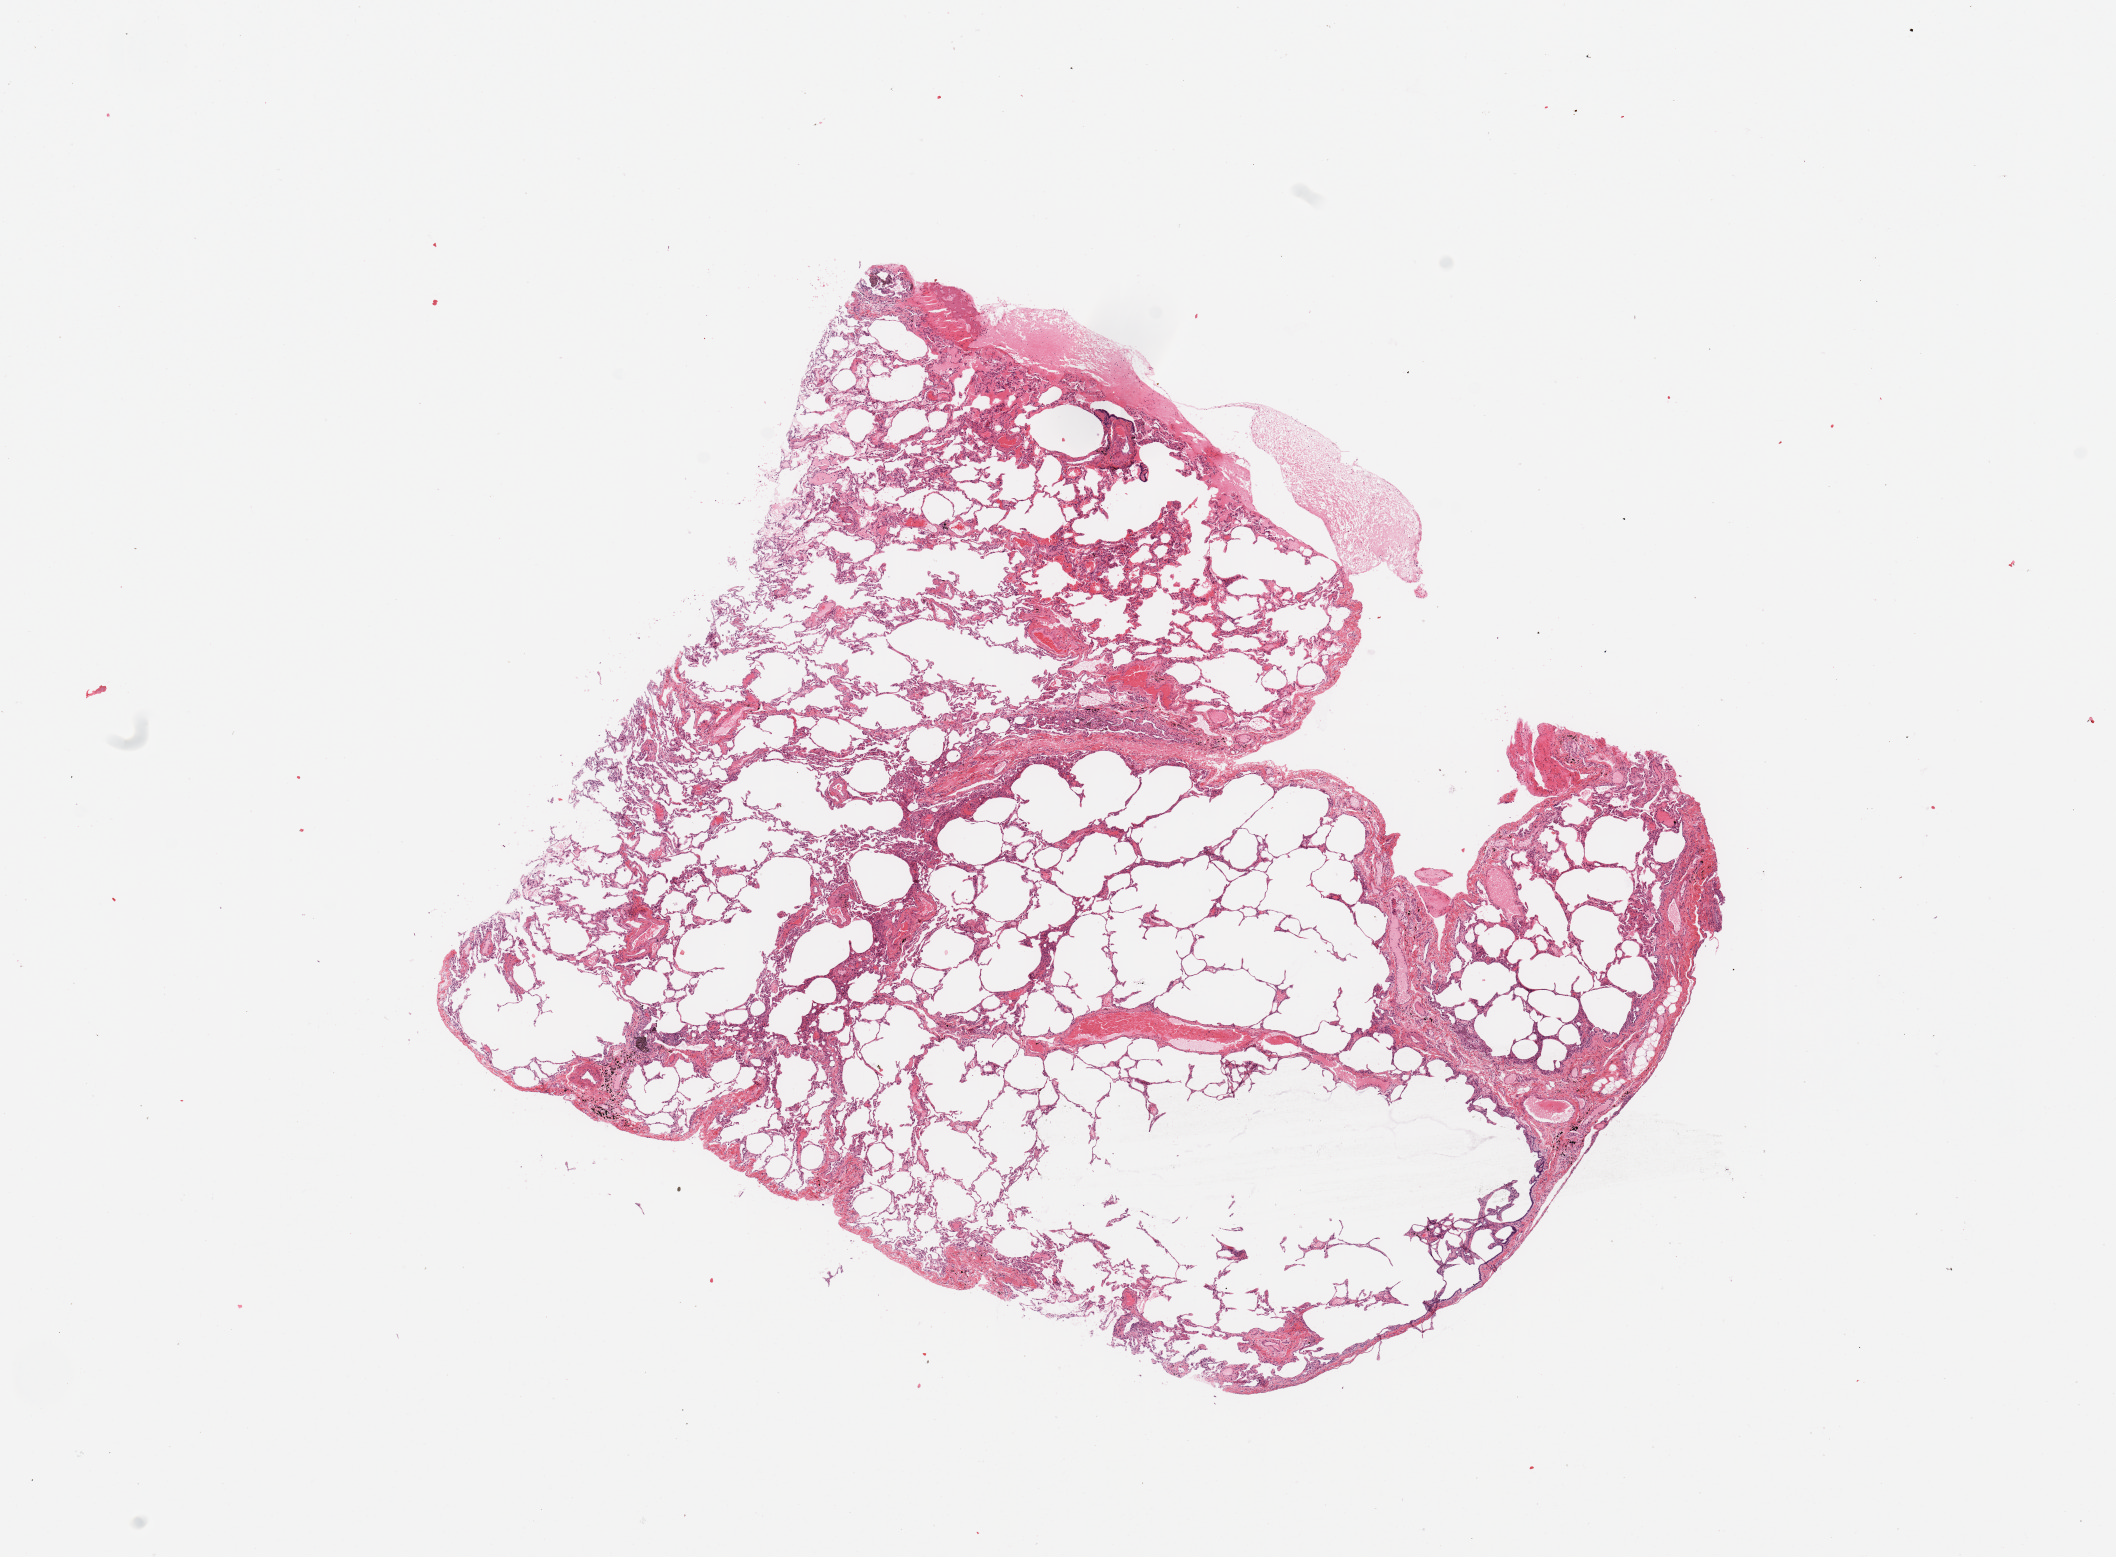
H&E-stained whole-slide image, low-resolution overview of the scanned area, about 16.7 x 12.3 mm (from a 20x scan). Normal (non-tumour) tissue sample, sampled site: lung. 53-year-old female patient.
This section: normal (non-tumour) tissue from the same patient. Patient diagnosis: Adenocarcinoma, NOS.